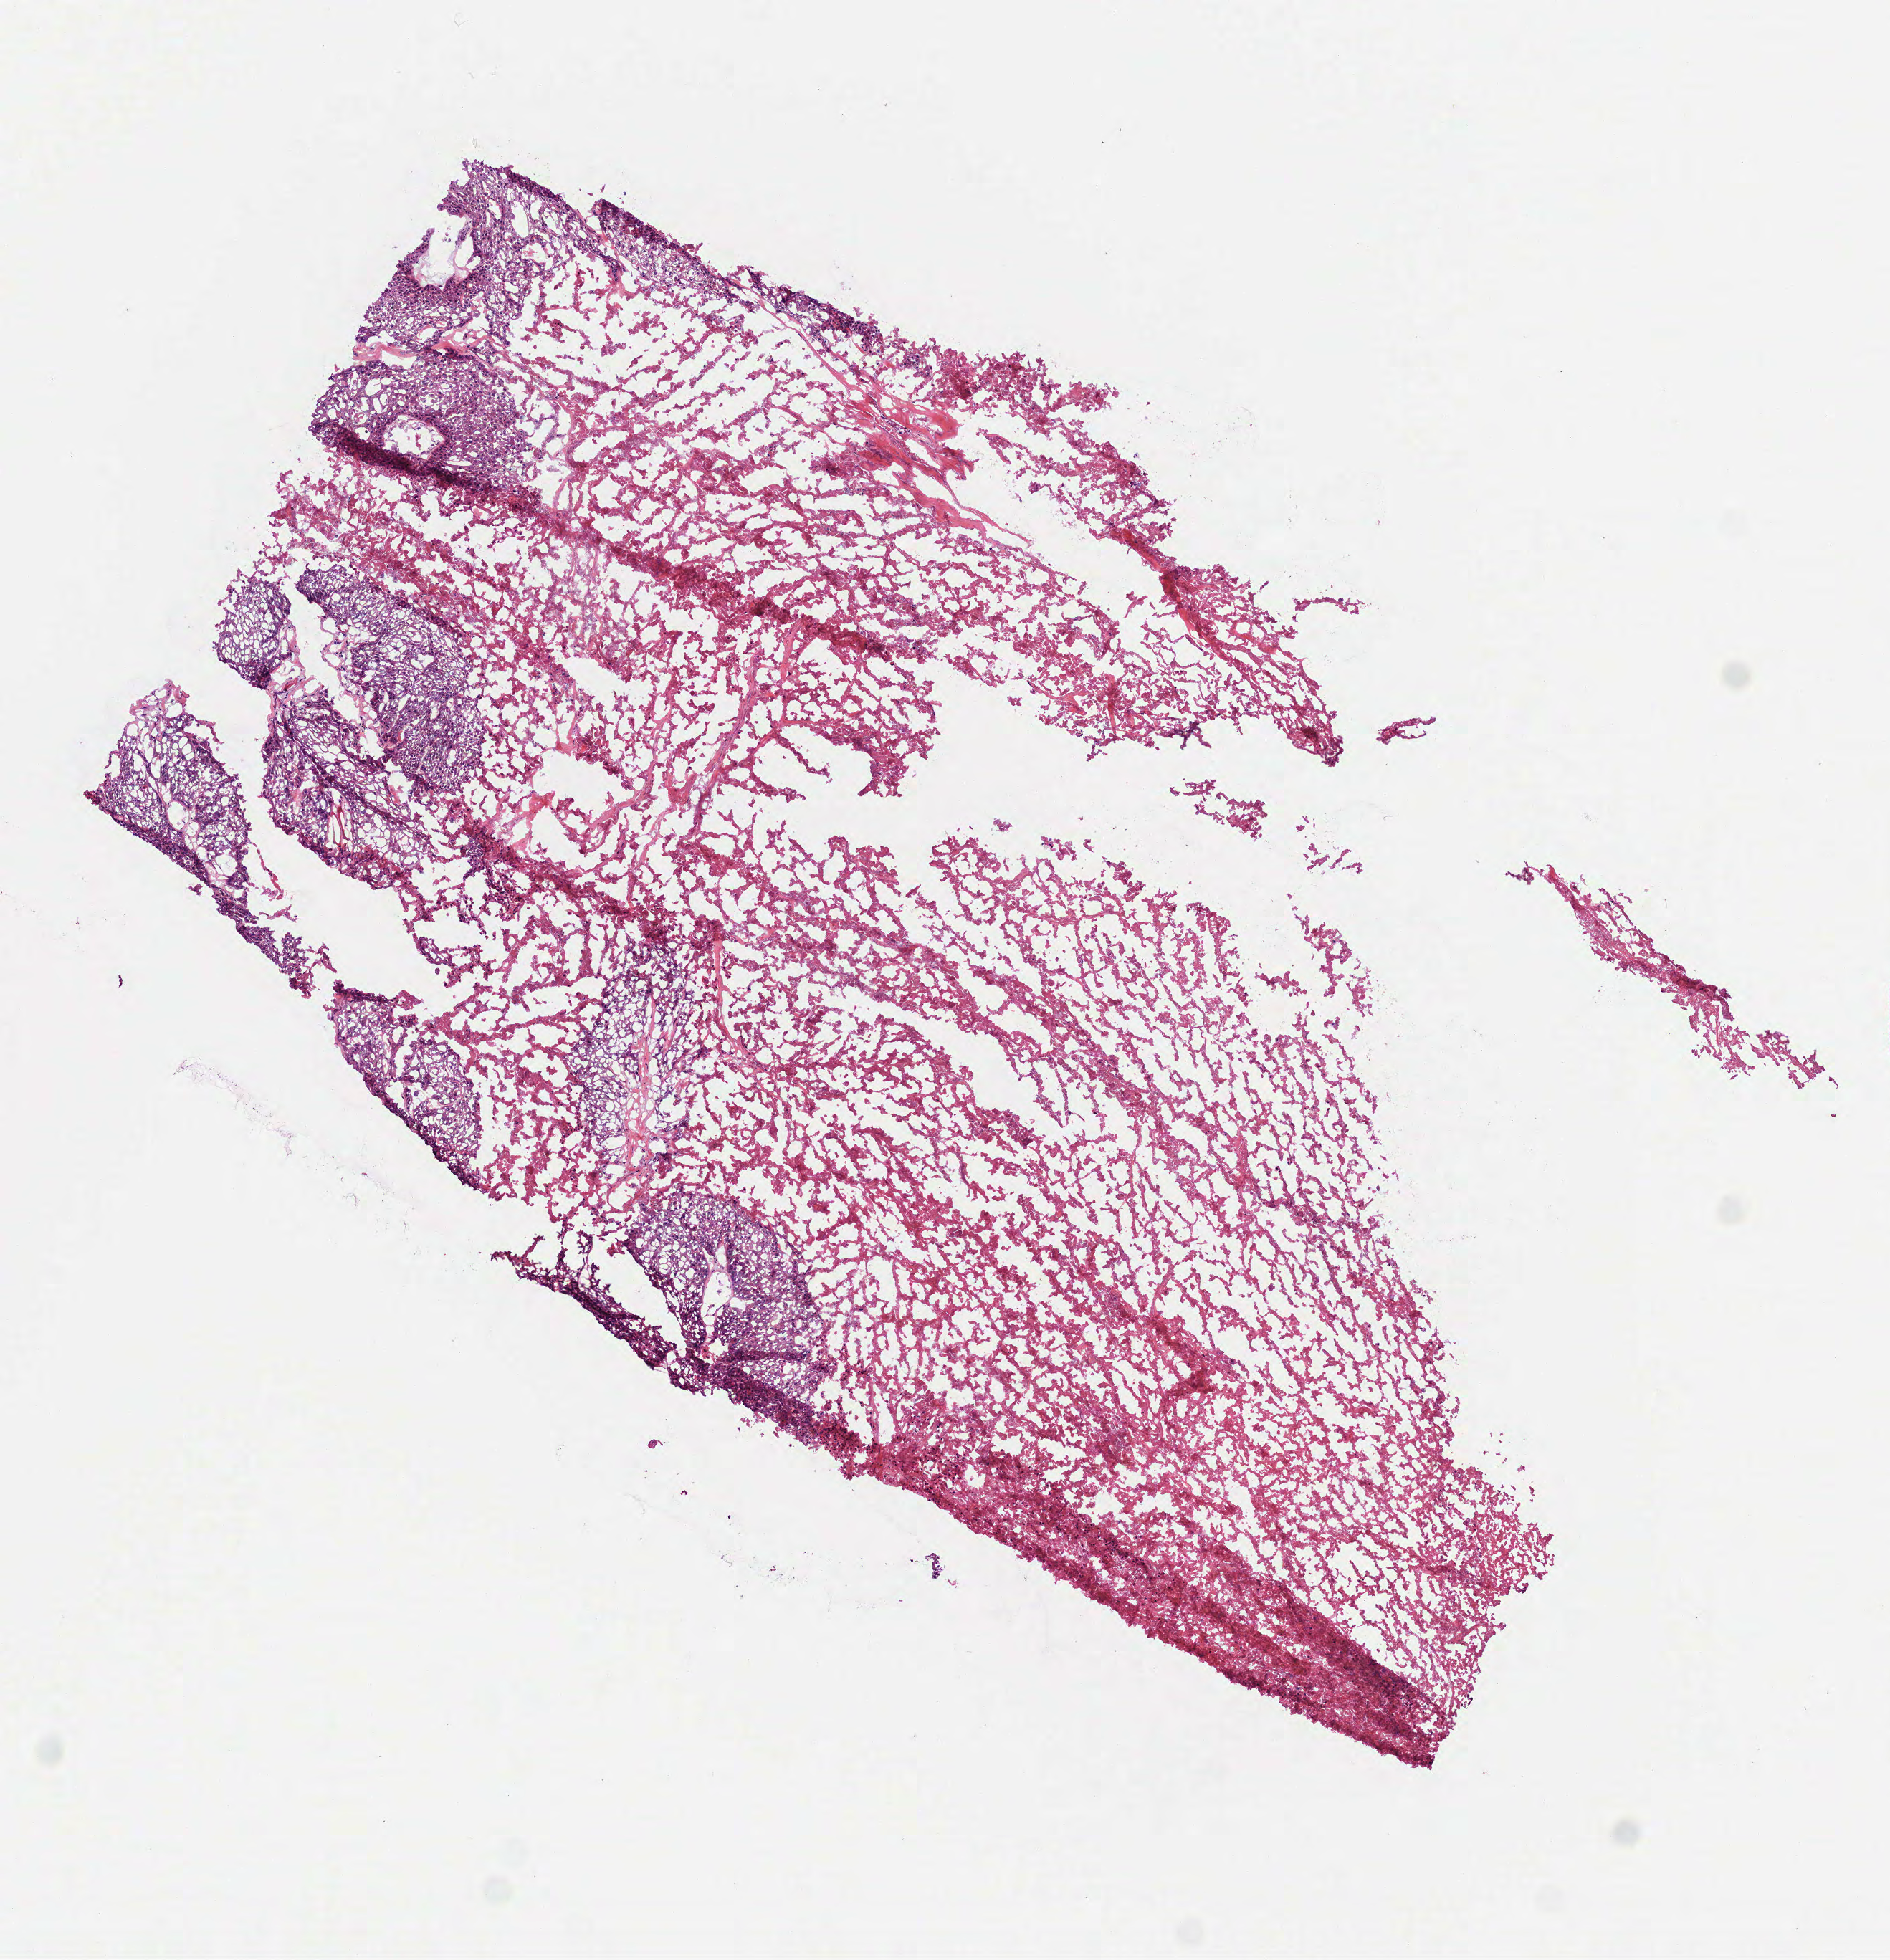
Whole-slide histology image, H&E-stained — whole scanned area (about 5.3 x 5.5 mm) shown as a low-resolution overview, frozen section from the bottom of the tissue portion, sample: primary tumour, head and neck. Male patient; age at initial diagnosis 58 years. Histologic grade: G2 (moderately differentiated). Composition of this section per pathologist review: tumour cells 25%, tumour nuclei 85%, normal cells 0%, stromal cells 75%, necrosis 0%.
AJCC pathologic stage: IVA (7th edition). TNM: T4a N0. Diagnosis: Squamous cell carcinoma, NOS (overlapping lesion of lip, oral cavity and pharynx).